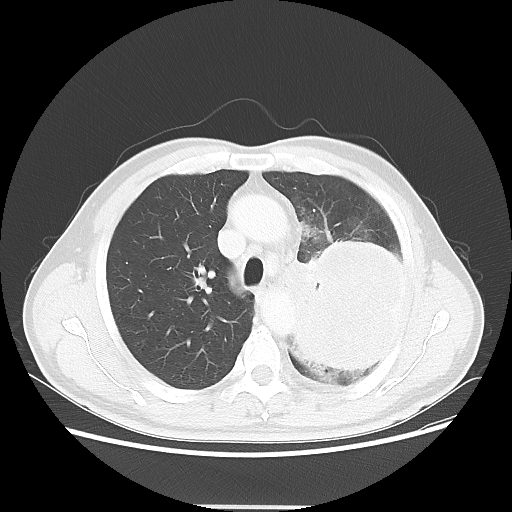
Chest CT, one axial slice. Slice 38 of 53 in the series (ordered by position). Reconstruction kernel LUNG. 100 kVp. Lung window (W 1500 / L -600 HU). 512 × 512 image matrix. Male patient, age 60 years. Case-level facts recorded for this patient, not image findings: clinical TNM (as recorded): T4 N1 M1a; histopathological grade: G3.
Outlined on this slice (bounding box drawn by a radiologist):
- lung tumour (recorded histology: large cell carcinoma): bounding box <292,227,412,387> (left, top, right, bottom; pixels)